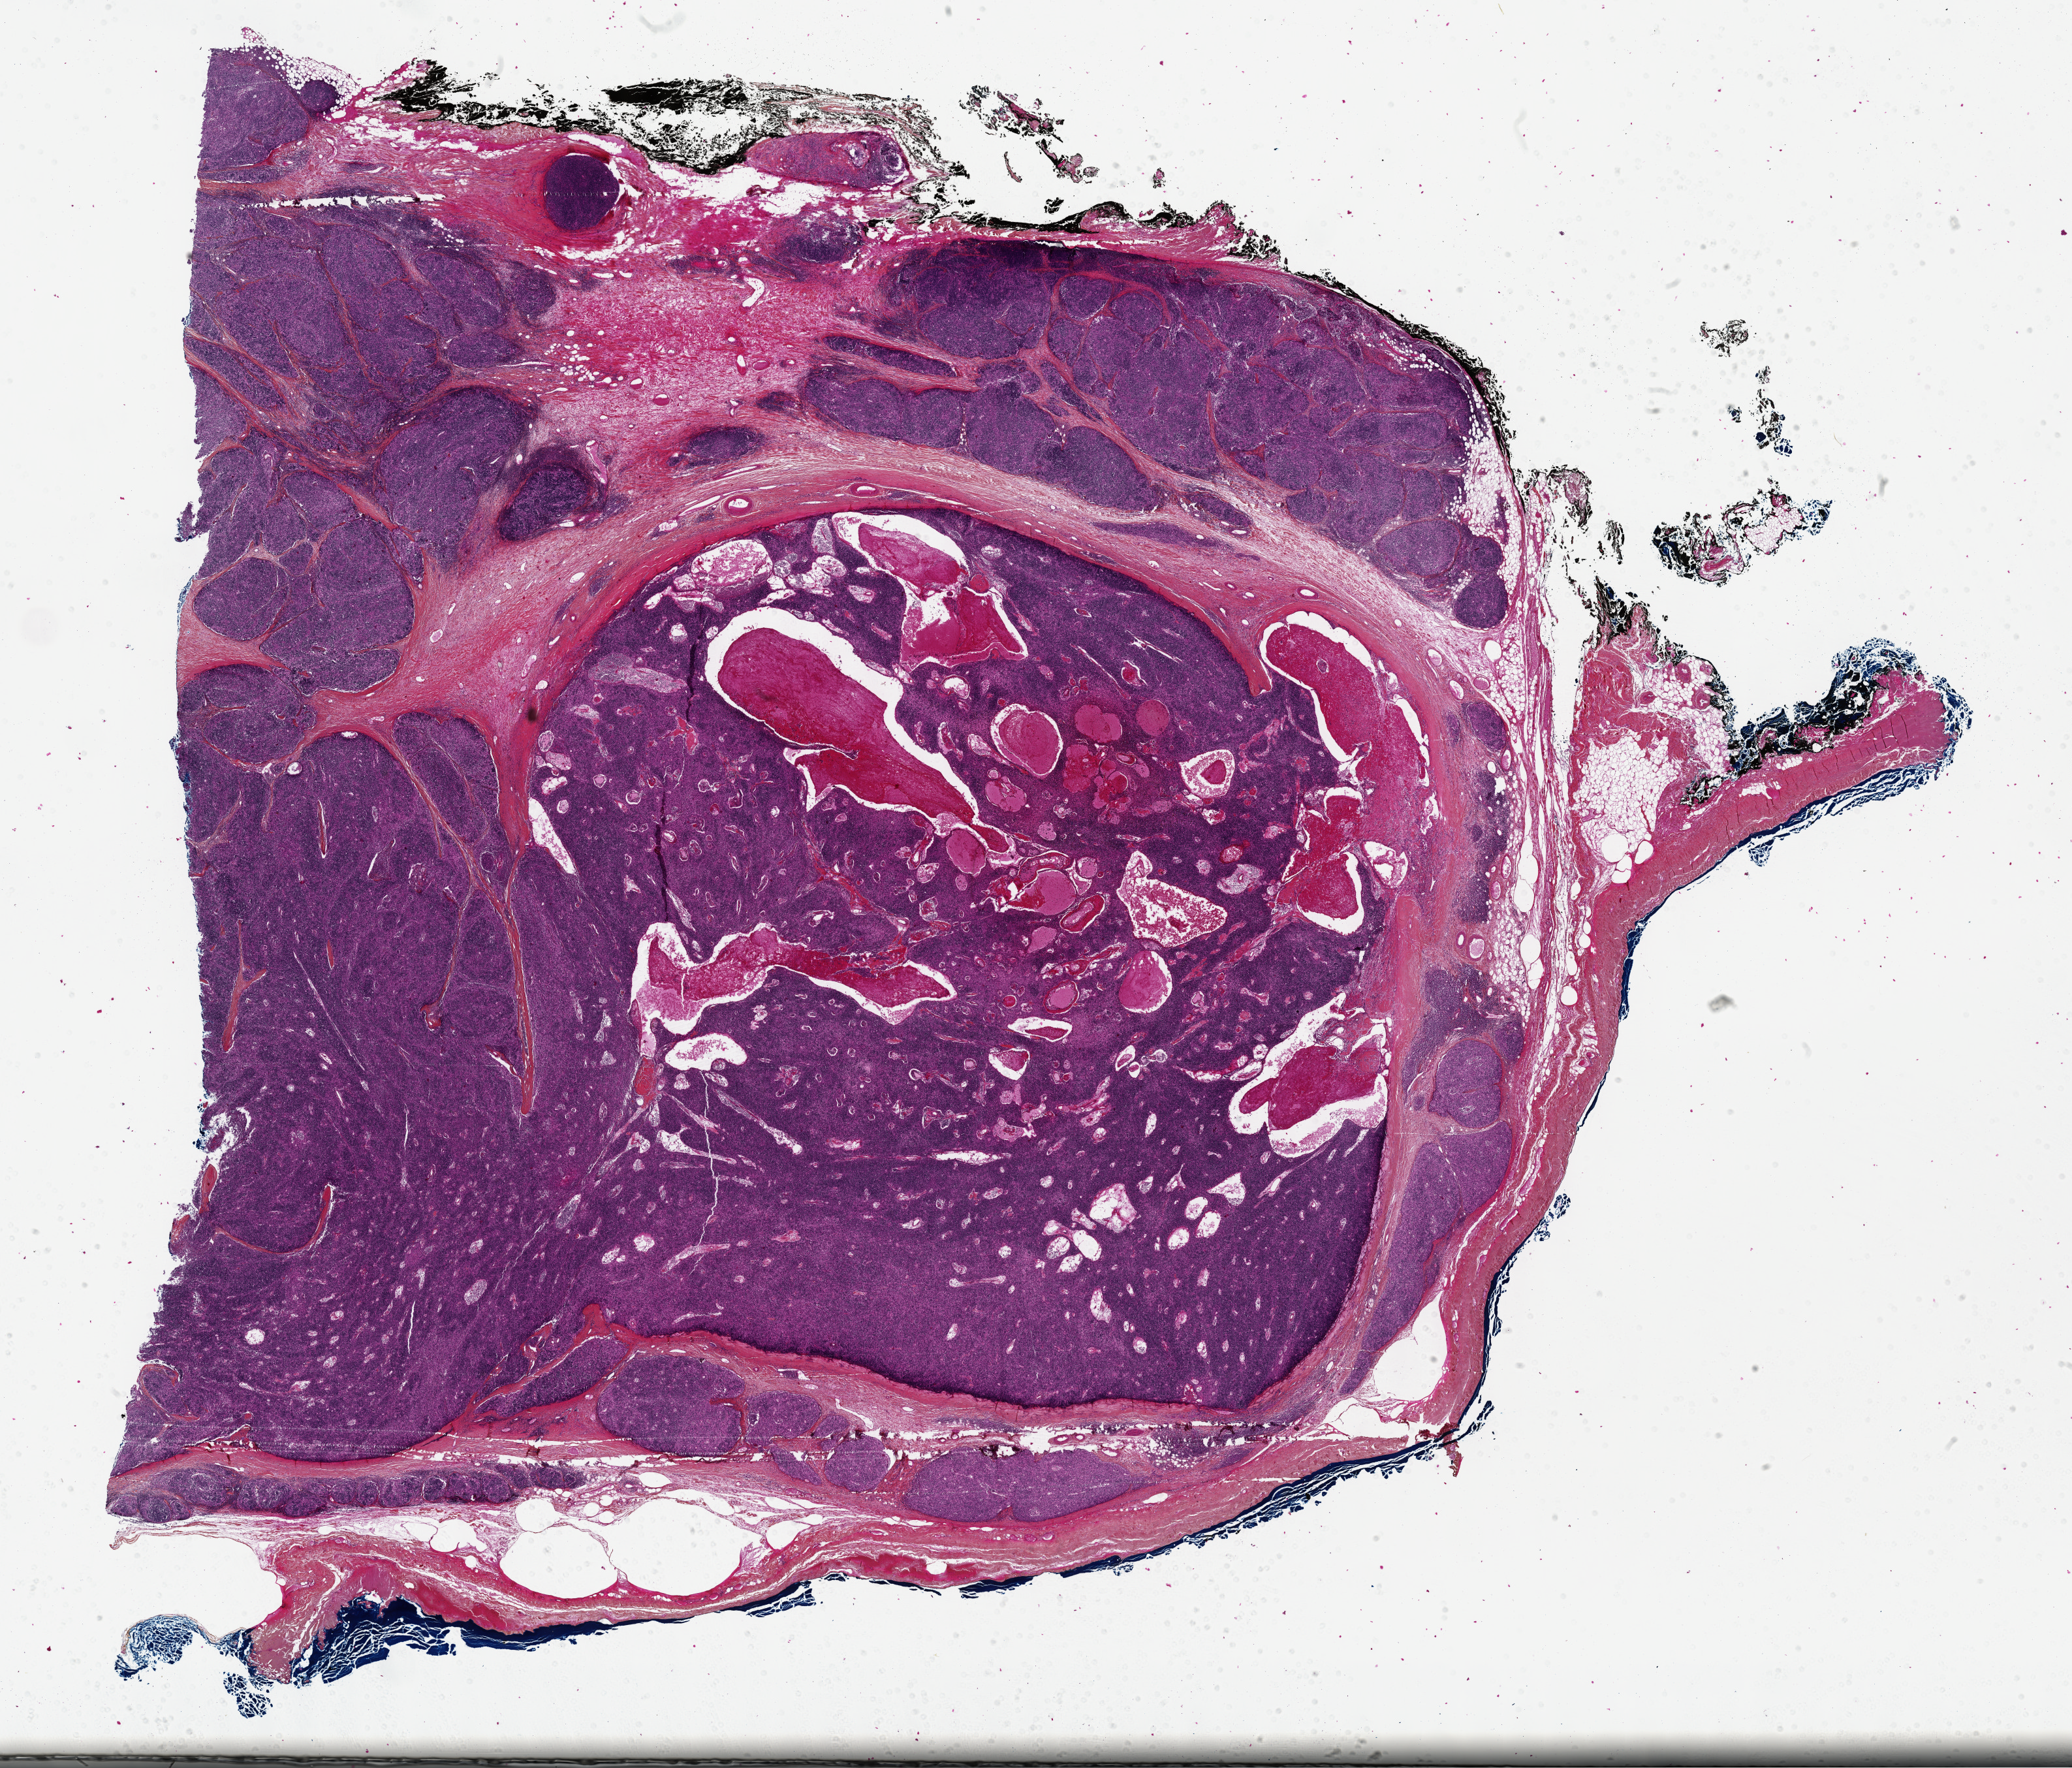
Whole-slide histology image, Hematoxylin and eosin (H&E) stained, low-resolution overview of the scanned area, about 25.7 x 21.9 mm (from a 40x scan). Formalin-fixed paraffin-embedded (FFPE) diagnostic section. Thymus, primary tumour sample. Male, age 68 years at initial diagnosis.
Pathologic diagnosis: Thymoma, type B2, malignant.